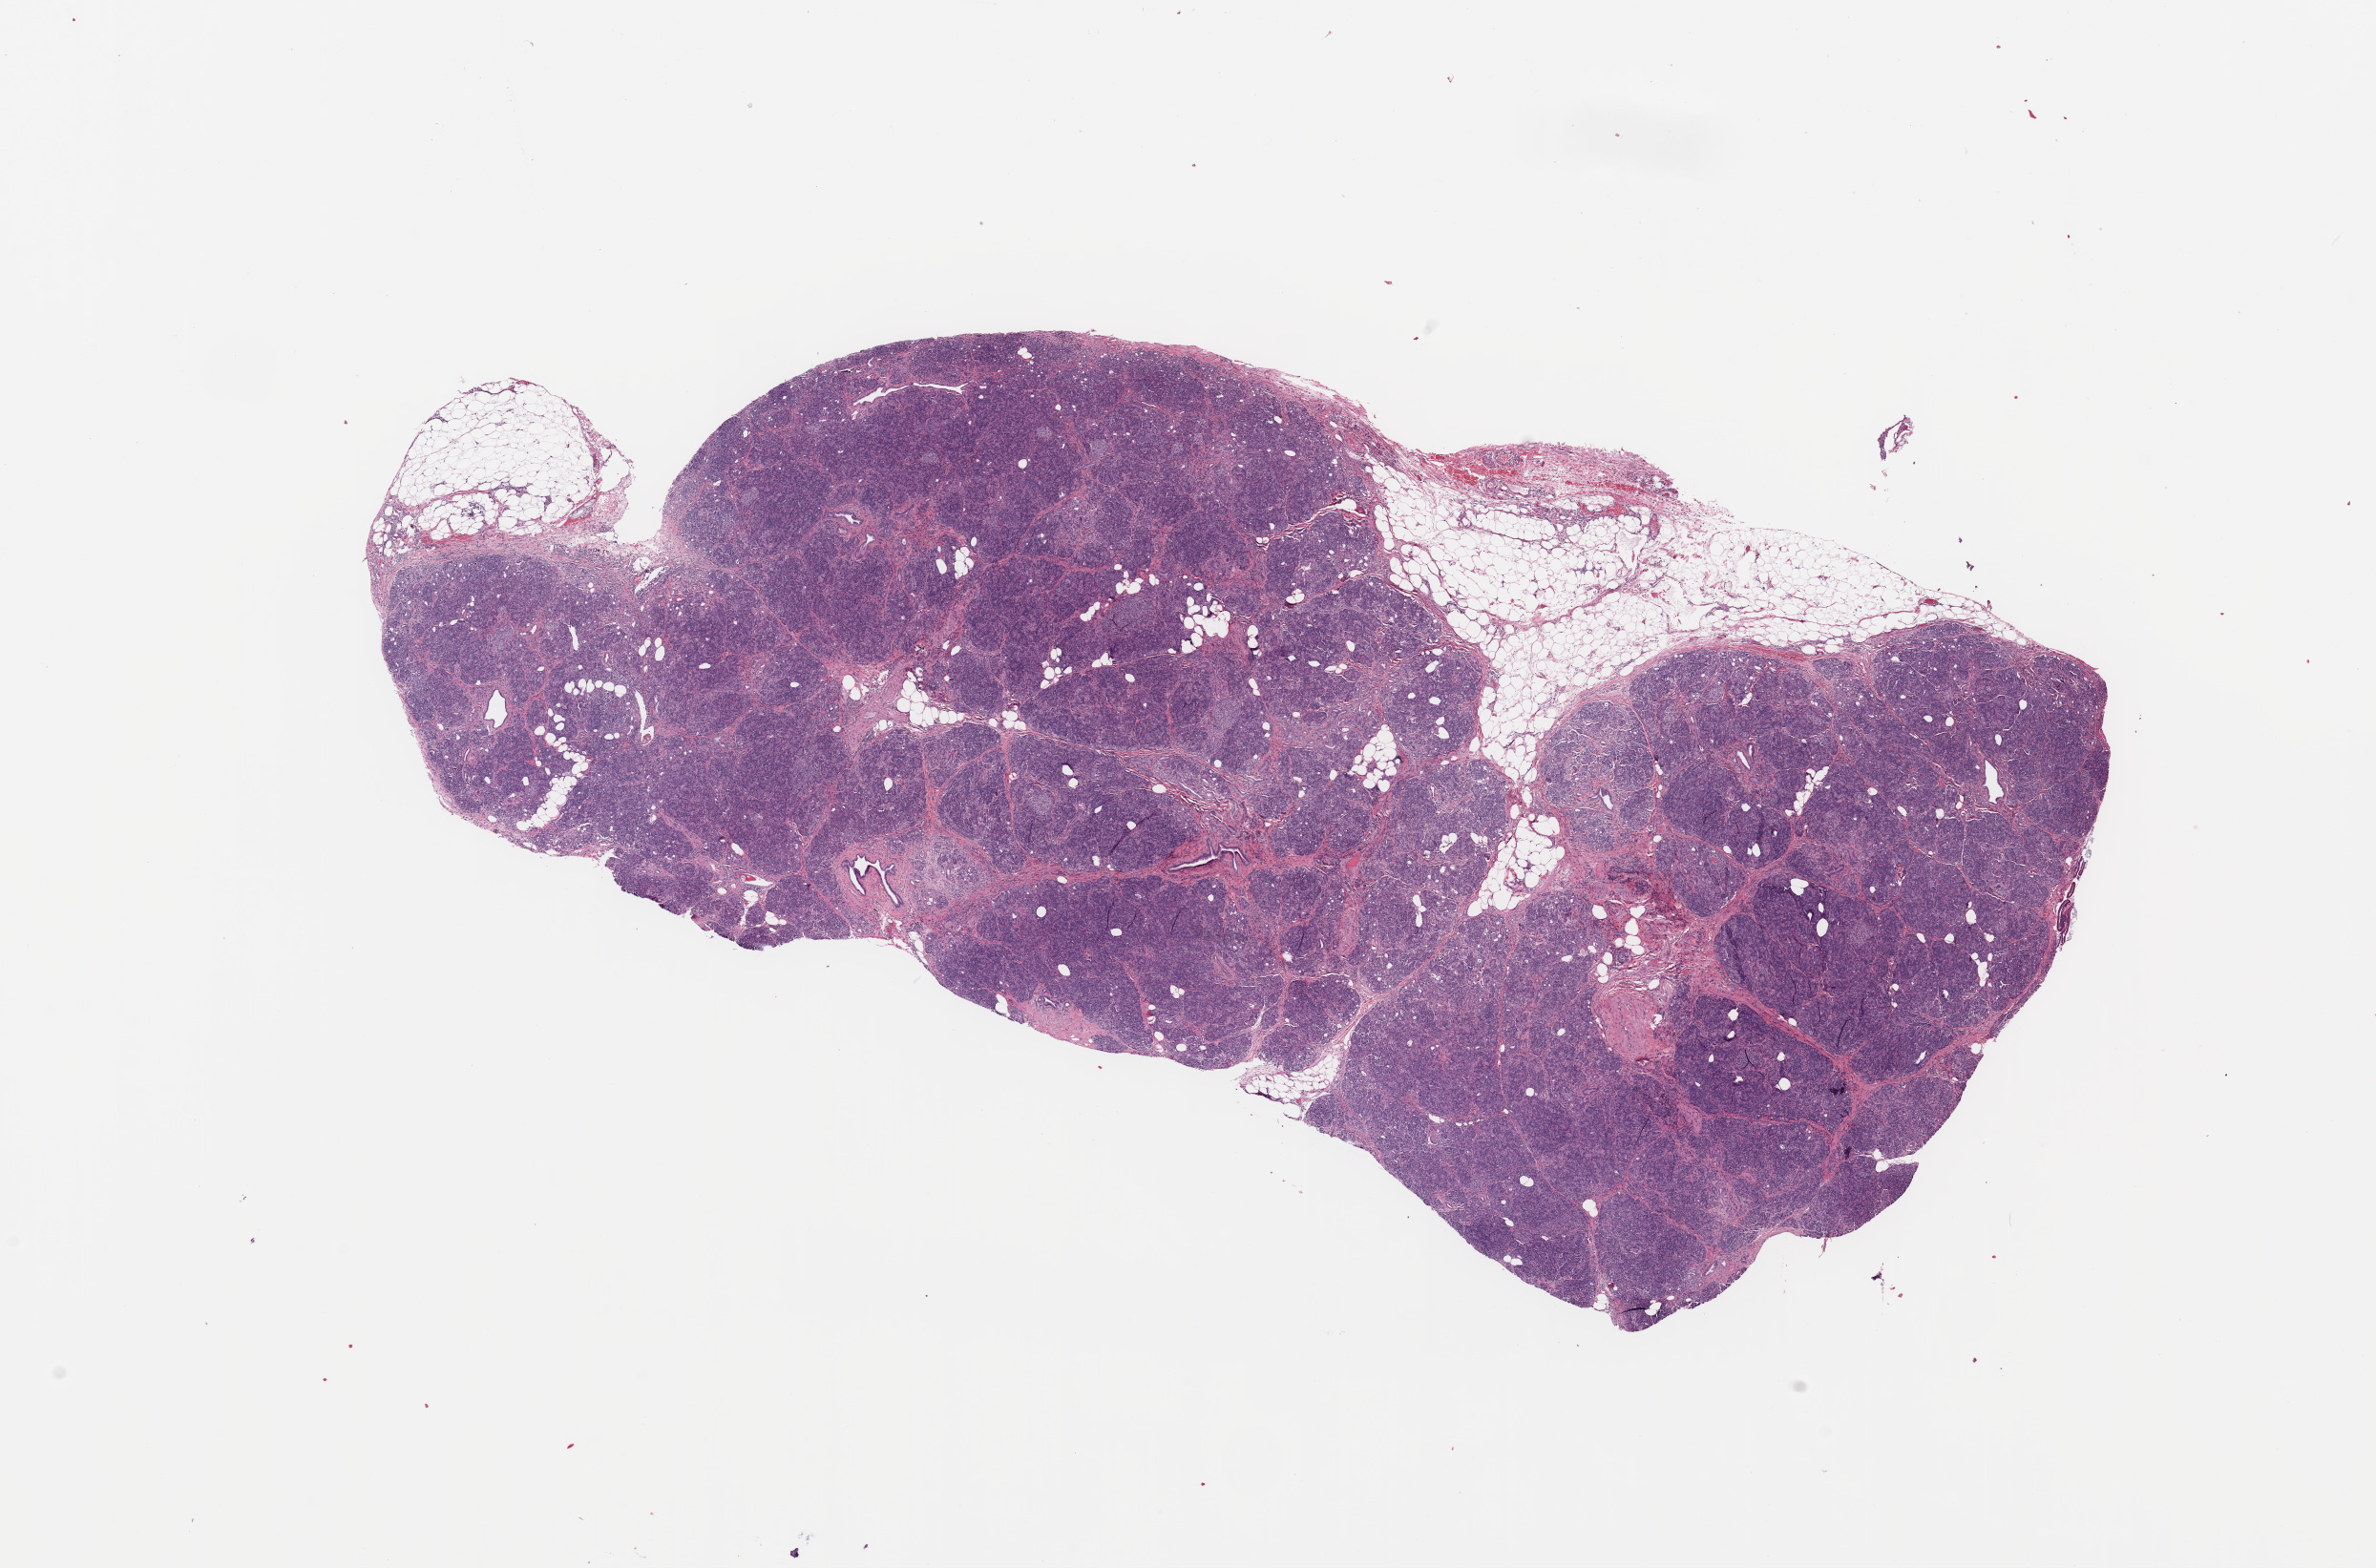
Whole-slide histology image, H&E-stained — whole scanned area (about 19.7 x 13.0 mm) shown as a low-resolution overview; normal (non-tumour) tissue sample, sampled site: pancreas. Patient: male, age 60 years.
- this section: normal (non-tumour) tissue from the same patient
- patient diagnosis: Infiltrating duct carcinoma, NOS